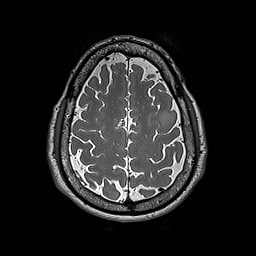
Brain MRI from a brain-tumour surgery series, one axial slice. Slice 63 of 192 in the series (ordered by position). 256 × 256 image matrix, field of view 250 × 250 mm. From the clinical record (not read from this slice): histopathology: Astrocytoma; WHO grade: 2; IDH mutation: yes; tumour location: Left Frontal.
Structures marked on this image (expert manual segmentation):
- tumour: bounding box <159,110,174,125> (left, top, right, bottom; pixels)